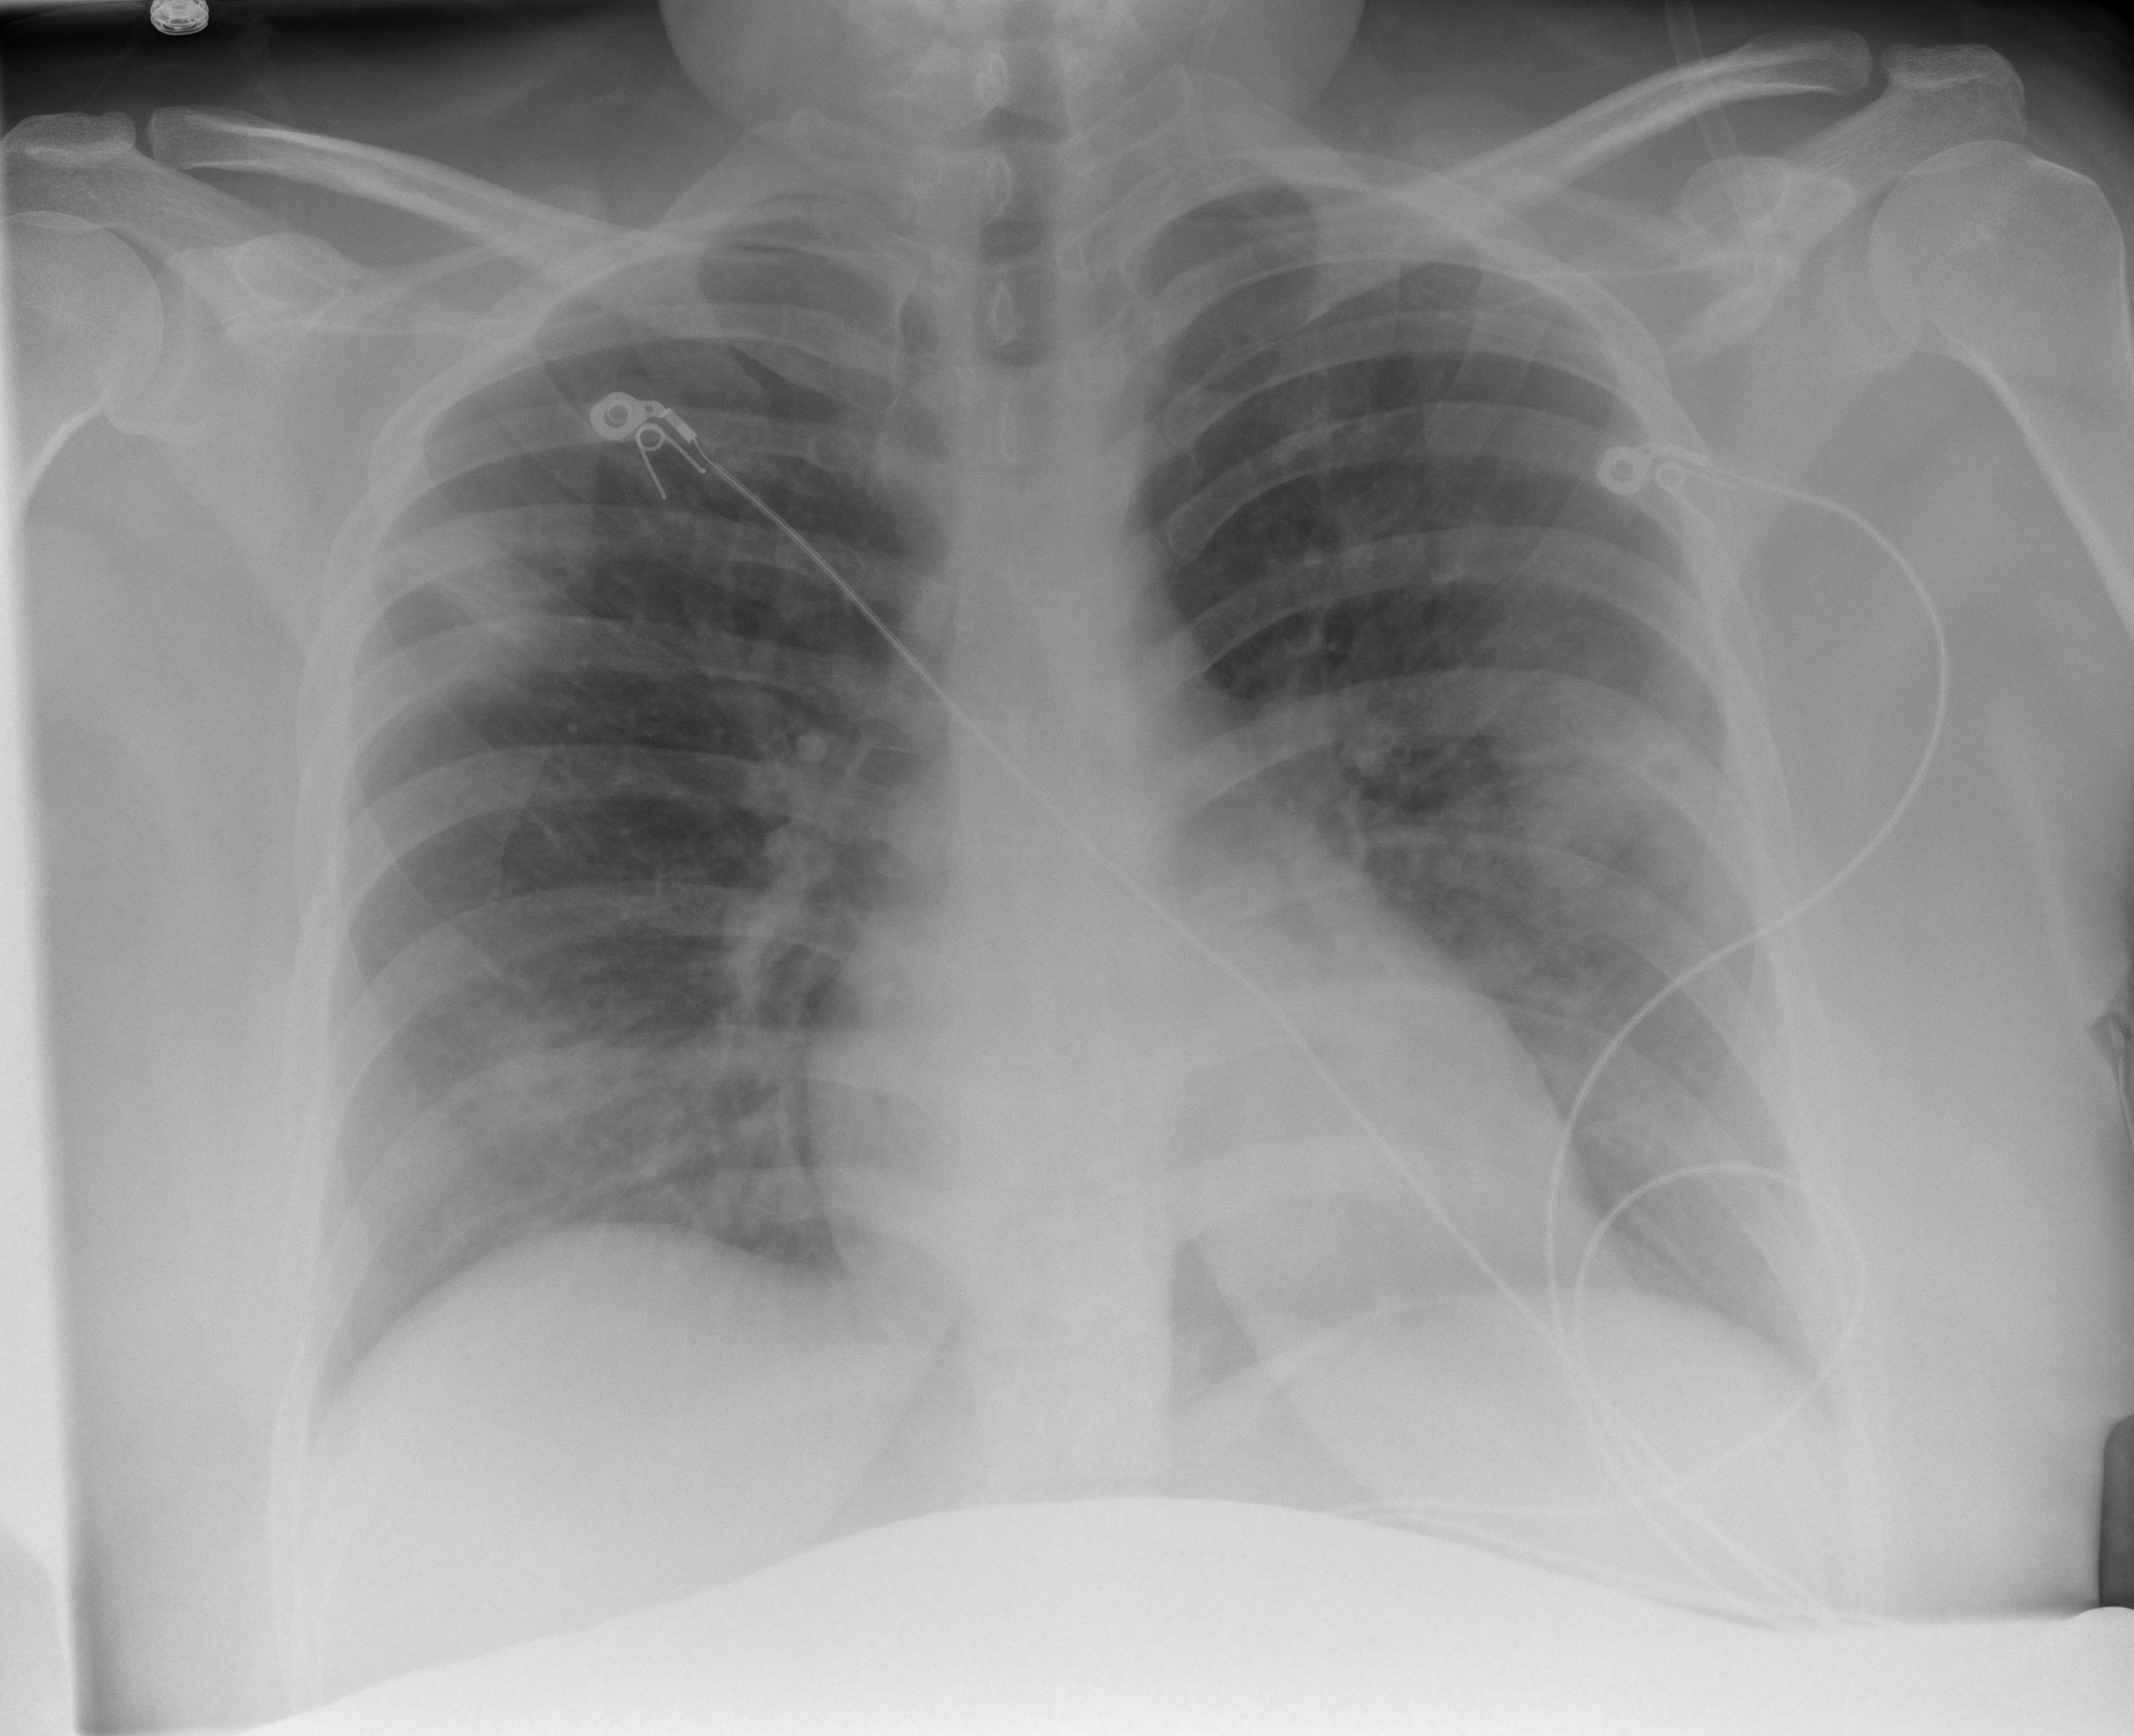
Portable chest radiograph, AP projection. Female patient, age 25 years; imaged 1 day after the COVID-19 diagnosis.
Radiologist's key findings for this exam: Patchy airspace opacities are seen in both lungs, involving the right upper and right lower lobe and left lower lobe.